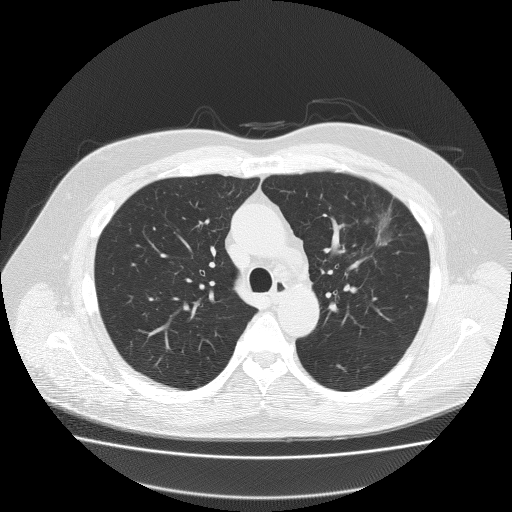
Axial slice from a low-dose chest CT screening exam; baseline screening round; lung window (W 1500 / L -600 HU); 2 mm slice thickness; slice 64 of 204 in the series. Male participant, aged 62 years at enrolment.
Expert reader's lesion annotation, box from (x=360, y=191) to (x=429, y=257) px. Reader record for this screening exam (exam-level; its link to the box is not recorded): non-calcified nodule or mass ≥4 mm, left upper lobe, 18 × 8 mm, spiculated (stellate) margins, soft tissue attenuation. Participant outcome: lung cancer diagnosed 49 days after this screen — bronchiolo-alveolar adenocarcinoma, NOS, left upper lobe, well differentiated (G1), stage IA (AJCC 6th edition), 25 mm at pathology.